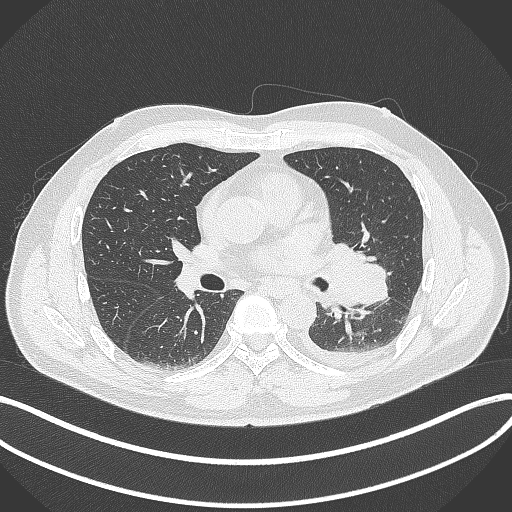
Chest CT, one axial slice. Position 191 of 342 along the scan axis. 120 kVp. Lung window (W 1500 / L -600 HU). 1 mm slice thickness. 512 × 512 image matrix, field of view 400 × 400 mm. Male patient, age 58 years. Case-level facts recorded for this patient, not image findings: clinical TNM (as recorded): T3 N1 M1b.
Structures marked on this image (rectangle marked by the reading radiologist):
- lung tumour (recorded histology: small cell carcinoma): bounding box (x1, y1, x2, y2) in pixels: (316, 232, 391, 318)